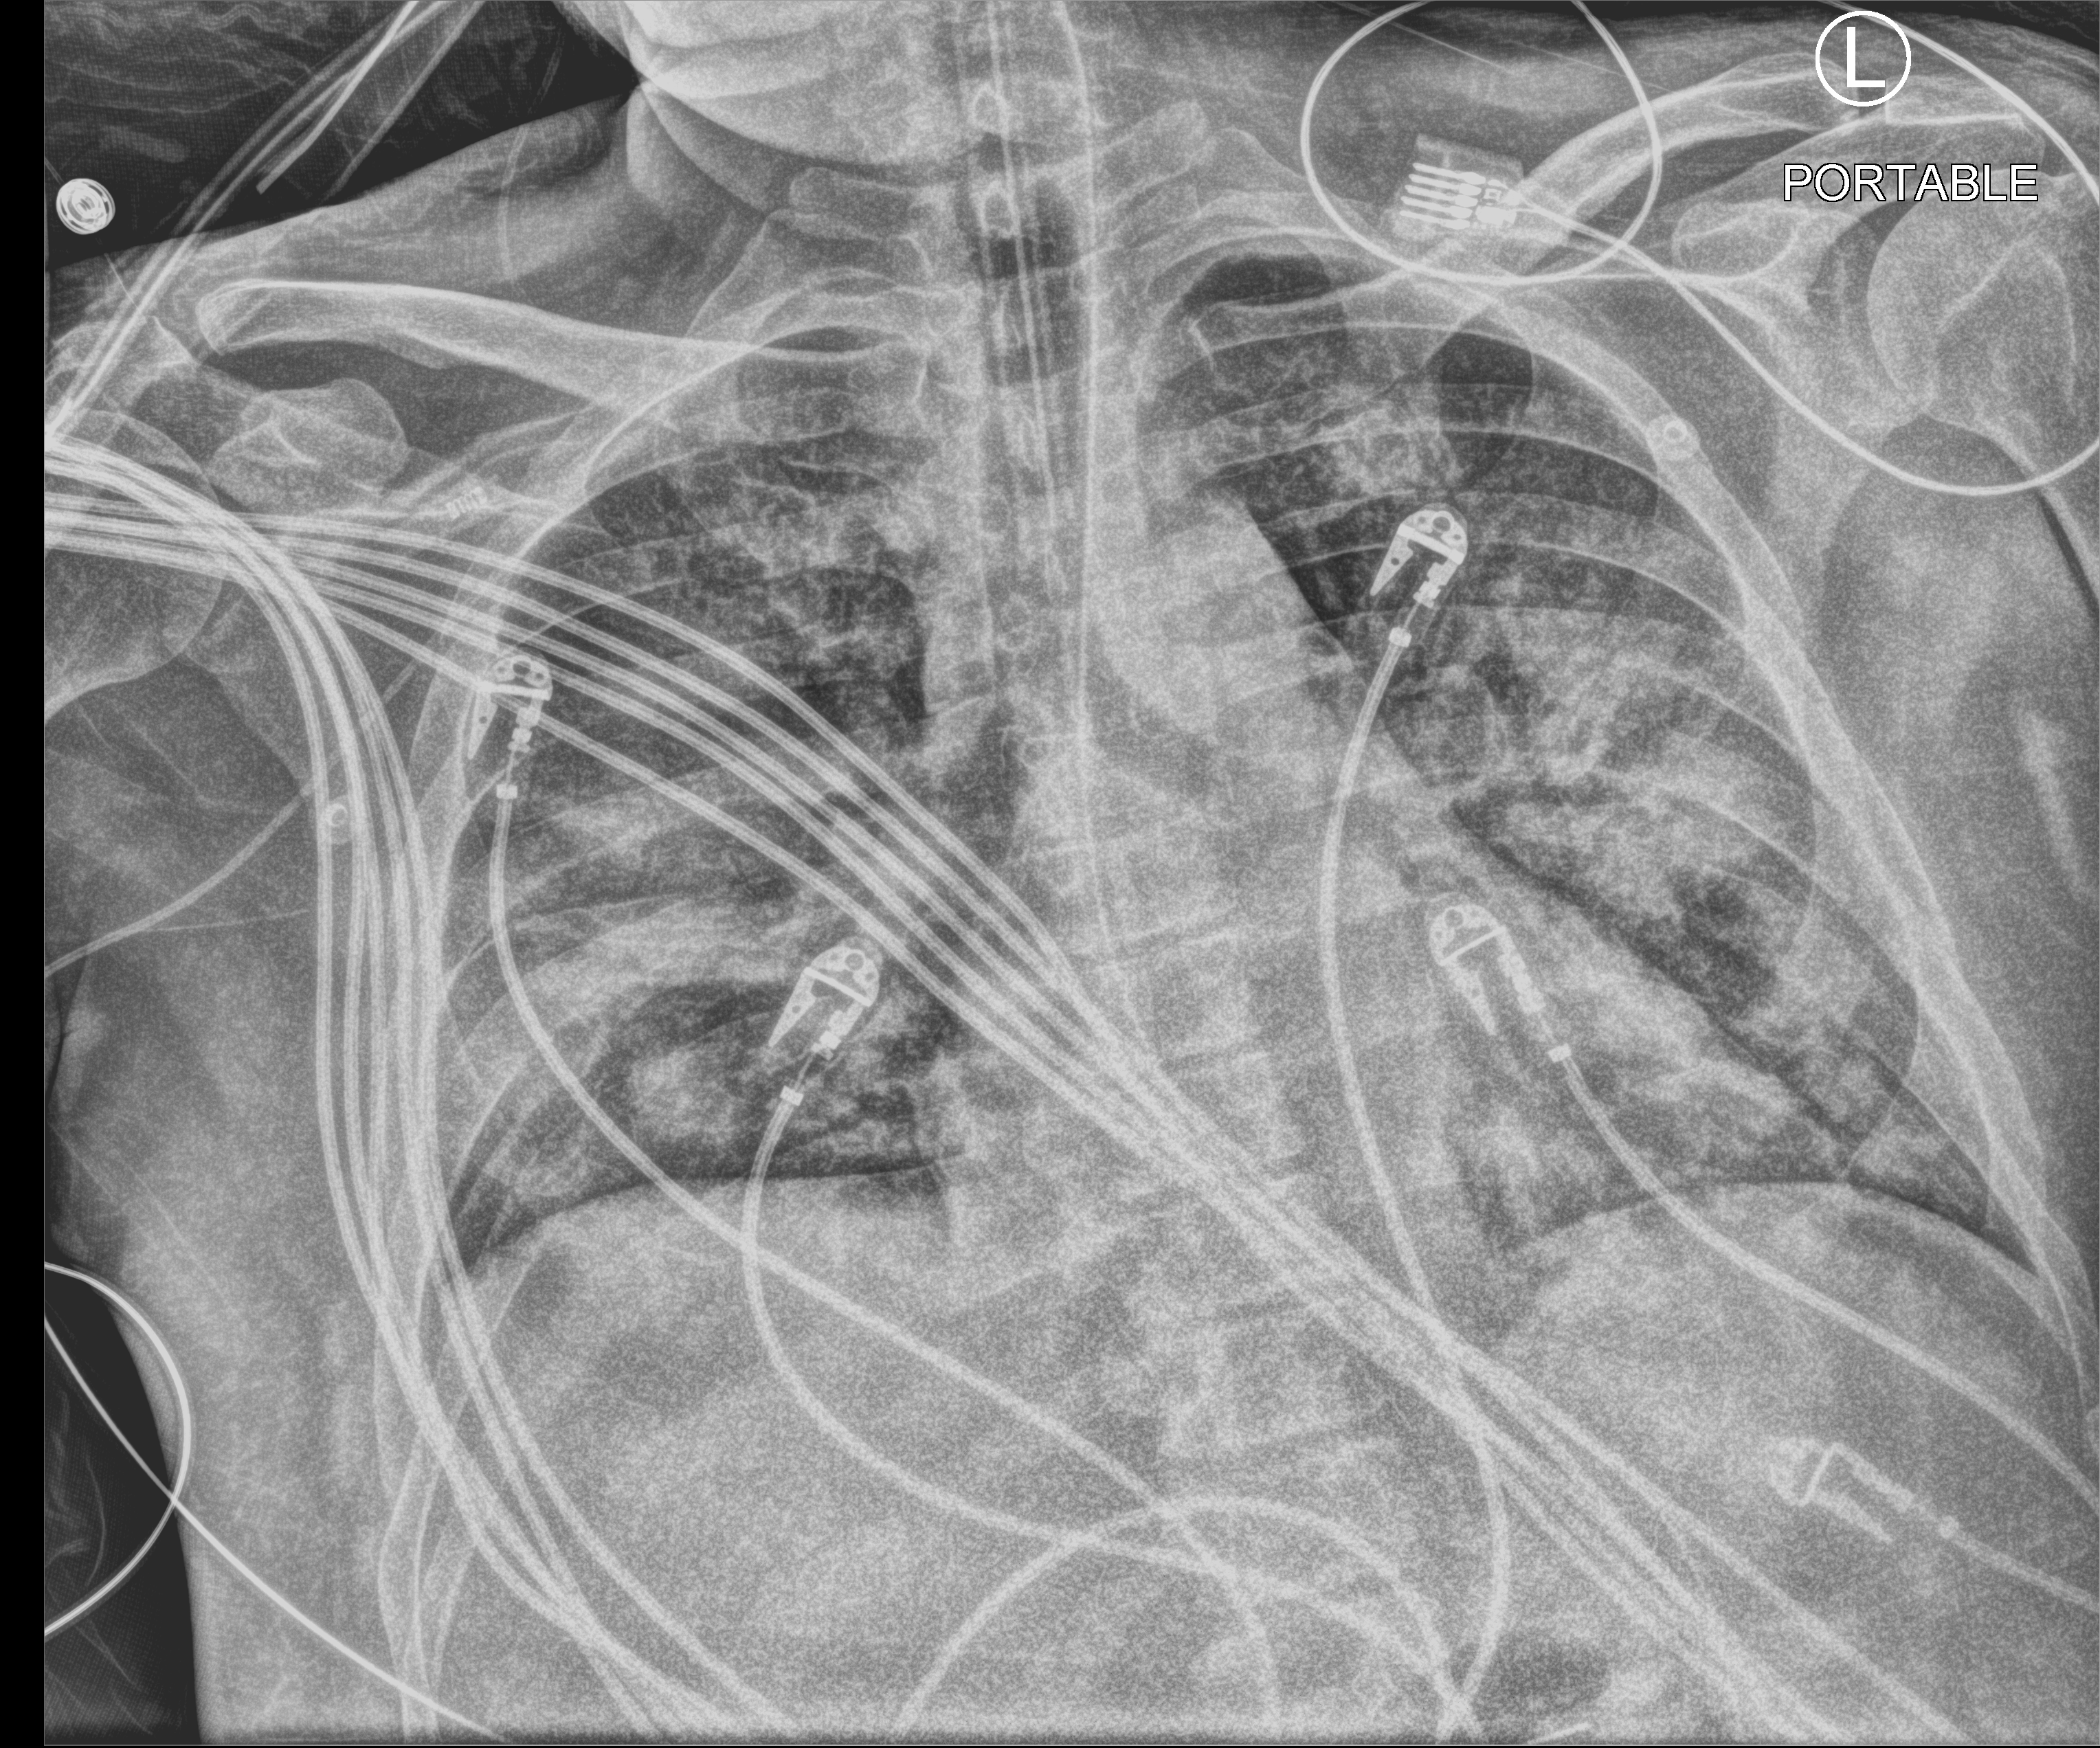
Portable chest radiograph; anteroposterior (AP) projection. Male patient hospitalised with COVID-19, age 18–59 years.
Admission-level facts for this patient (not findings on this image; timing relative to this image not recorded):
- mechanically ventilated during this hospital stay: yes
- length of hospital stay: 20 days
- admitted to intensive care during this hospital stay: yes